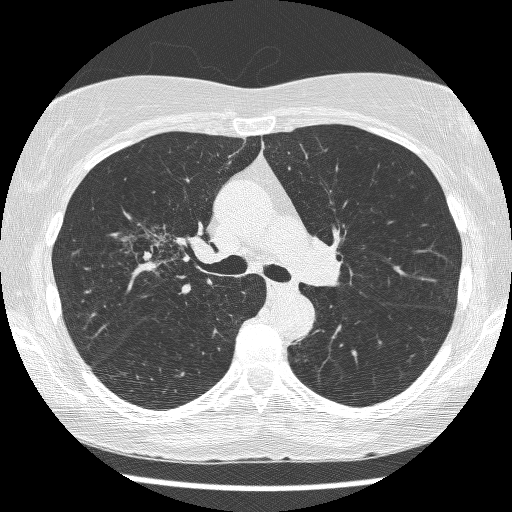
Chest CT (low-dose screening protocol), one axial image, baseline annual screen, lung window (W 1500 / L -600 HU), lung (sharp) reconstruction kernel (BONE), 512 × 512 image matrix, field of view 316 × 316 mm. Female, age 64 years at enrolment. Former smoker at enrolment.
Expert-annotated lung lesion, bounding box (x1, y1, x2, y2) in pixels: (125, 222, 204, 292). The screening reader recorded 3 non-calcified nodules or masses ≥4 mm on this exam (right upper lobe, right upper lobe, left lower lobe); which of them this box marks is not recorded. Official screen result: positive, change unspecified: nodule(s) >= 4 mm or enlarging nodule(s), mass(es), or other non-specific abnormalities suspicious for lung cancer. Lung cancer was diagnosed 735 days after this screen: adenocarcinoma, NOS, right upper lobe, right middle lobe, right hilum, stage IV (AJCC 6th edition), 85 mm at pathology.